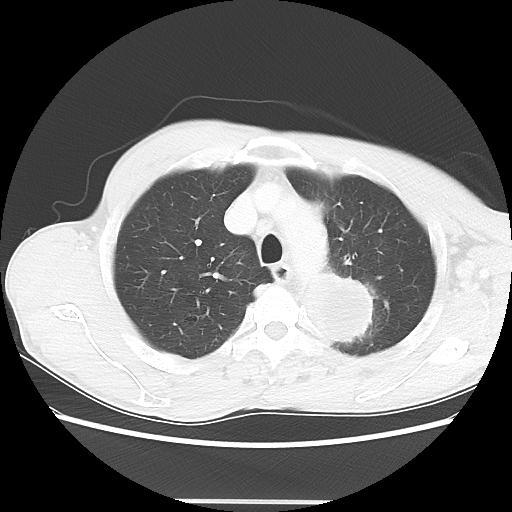
Chest CT, one axial slice; position 51 of 62 along the scan axis; 100 kVp; lung window (W 1500 / L -600 HU); 512 × 512 image matrix. Patient: male, 61 years. From the clinical record (not read from this slice): clinical TNM (as recorded): T3 N1 M1.
Outlined on this slice (bounding box drawn by a radiologist):
- lung tumour (recorded histology: adenocarcinoma): bounding box [x1, y1, x2, y2] px = [295, 271, 381, 352]